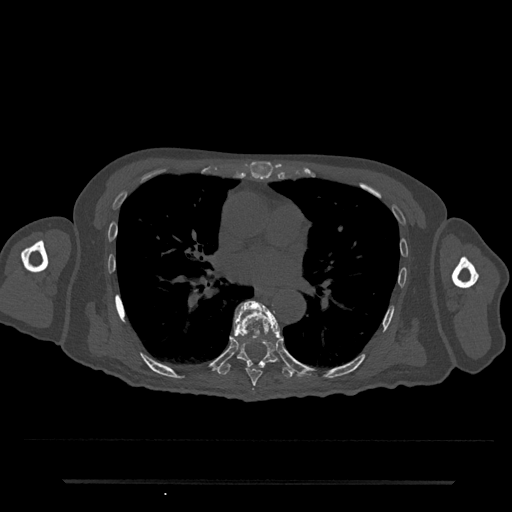
CT including the spine, one axial slice; position 452 of 797 along the scan axis; 120 kVp; bone window (W 1800 / L 400 HU); 512 × 512 image matrix. Male patient, age 74 years. From the clinical record (not read from this slice): primary cancer: prostate.
Annotated regions visible in this slice (semi-automatic segmentation, software-assisted and operator-edited):
- T7 vertebra: bounding box (x1, y1, x2, y2) in pixels: (233, 301, 282, 386)
- T8 vertebra: (216, 301, 294, 379)